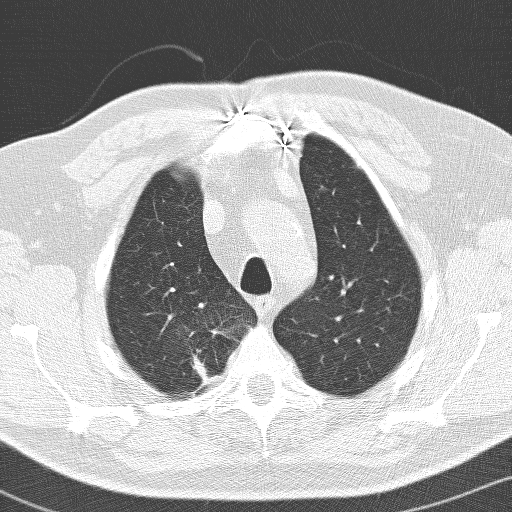
Low-dose screening chest CT, one axial slice. Position 118 of 141 along the scan axis. 120 kVp. Lung window (W 1500 / L -600 HU). 3.2 mm slice thickness. 512 × 512 image matrix, field of view 326 × 326 mm.
Annotated regions visible in this slice (expert manual segmentation):
- lesion 1 (tumor, upper lobe of right lung): box from (x=193, y=333) to (x=225, y=381) px